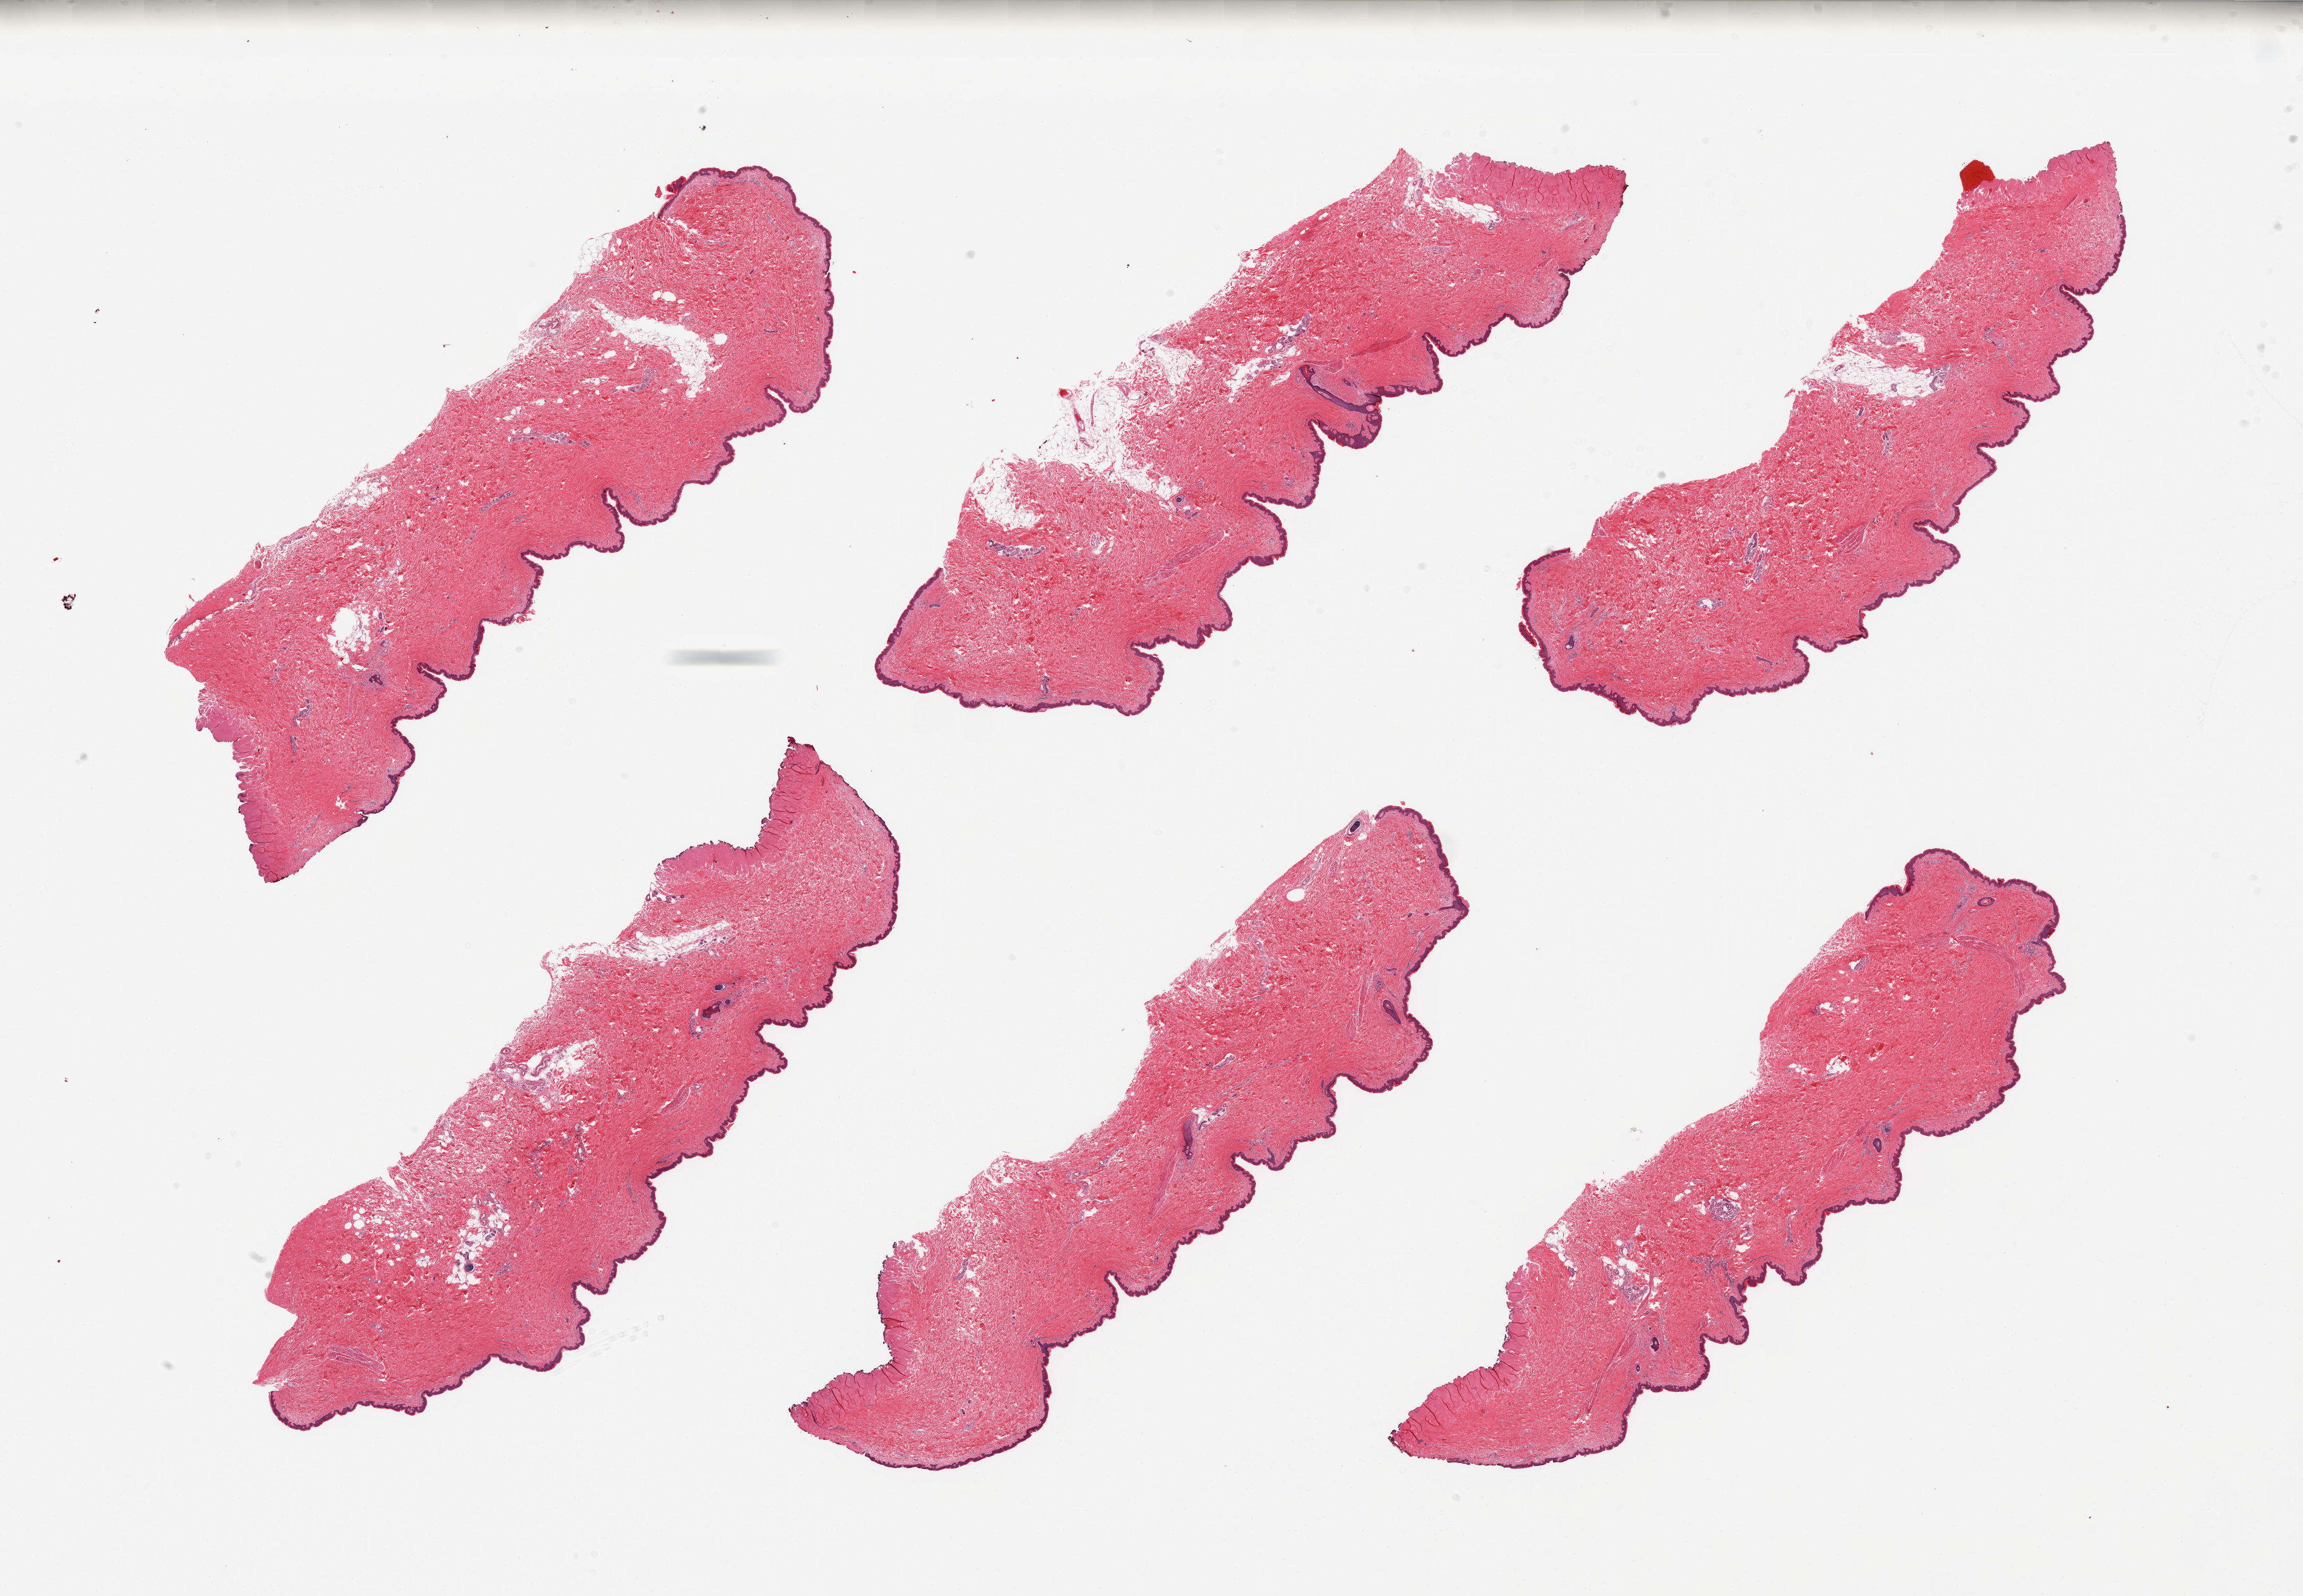
Whole-slide image, H&E stain, shown as a low-resolution overview of the whole scanned area (about 31.5 x 21.8 mm), PAXgene-fixed, paraffin-embedded tissue, section of skin of suprapubic region (target tissue), donor tissue sample.
* review note (as recorded): 6 pieces, minimal dermal fat, squamous epithelium is ~40-50 microns